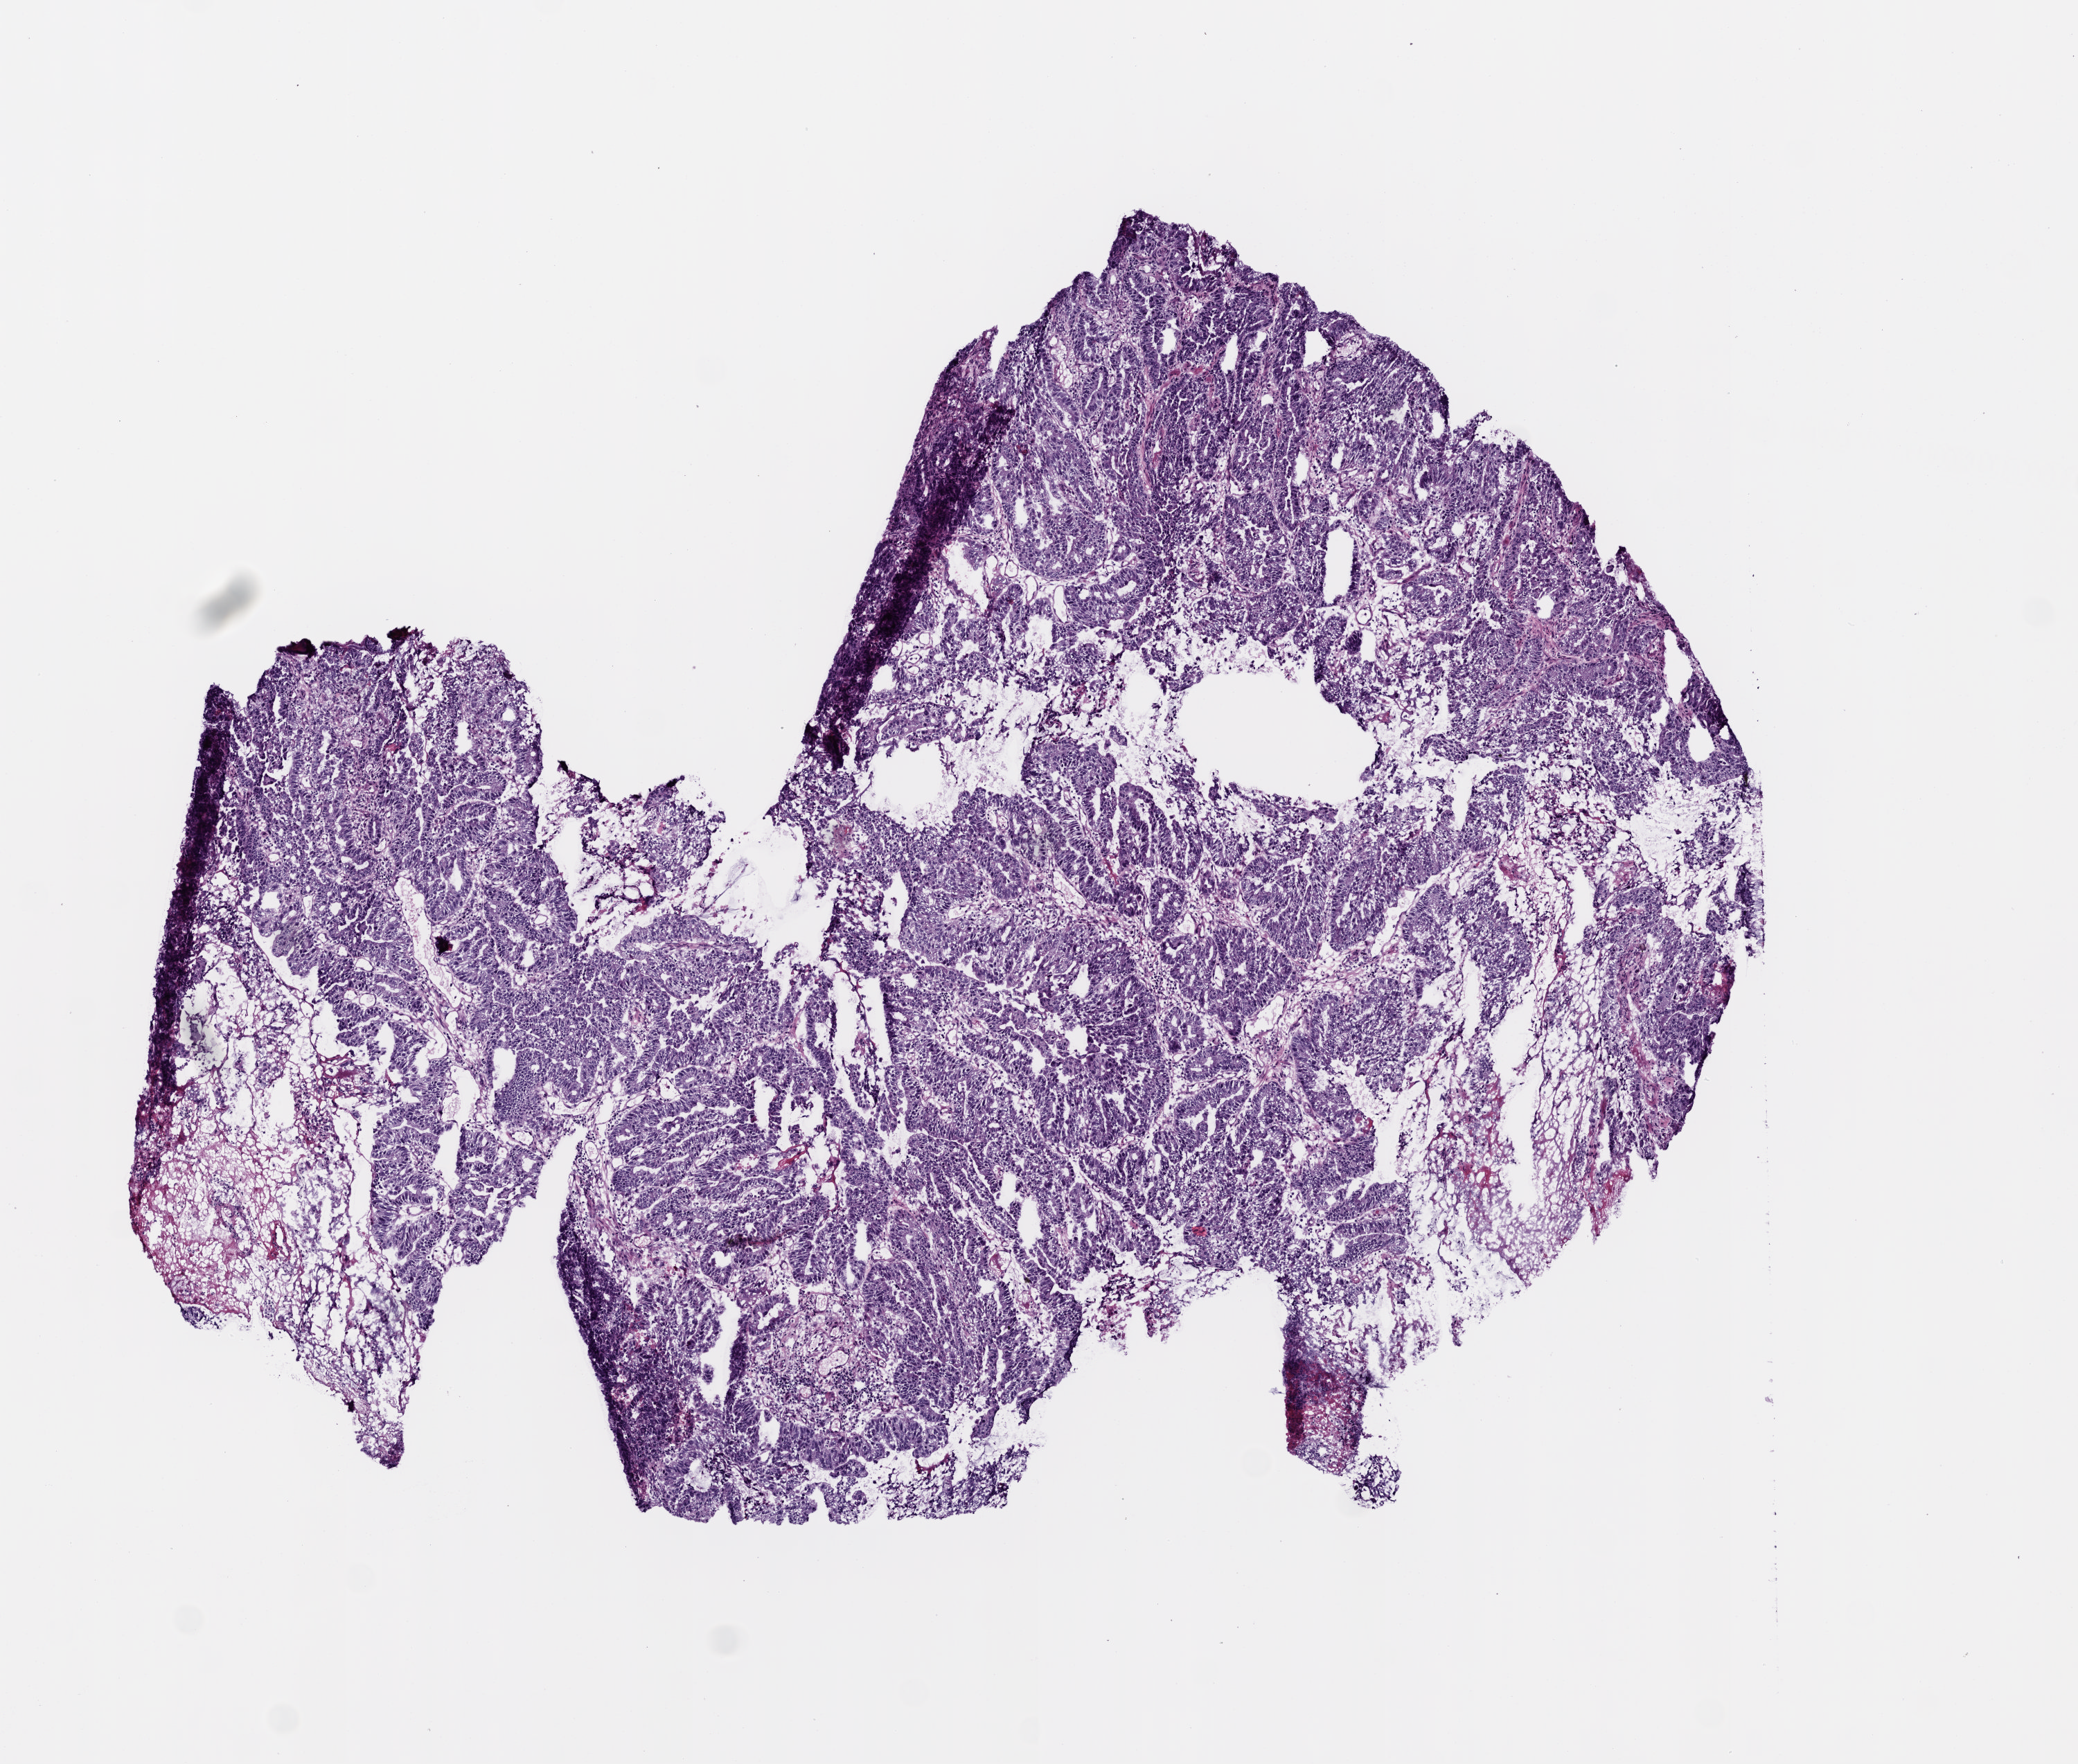
Hematoxylin and eosin (H&E) stained whole-slide image — shown as a low-resolution overview of the whole scanned area (about 6.0 x 5.1 mm). Frozen section from the top of the tissue portion. Primary tumour sample from the stomach. Female patient; age at initial diagnosis 81 years. Pathologist review of this section (percent, as recorded): tumour cells 82%, tumour nuclei 75%.
Histologic diagnosis: Adenocarcinoma, intestinal type (cardia, NOS).